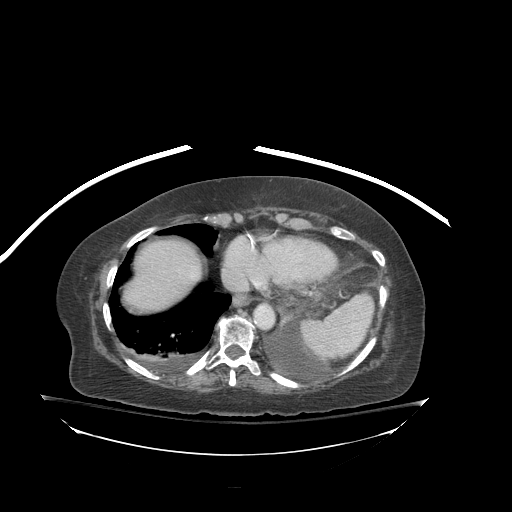
Contrast-enhanced abdominal CT (liver protocol), one axial slice. Position 77 of 81 along the scan axis. Soft-tissue window (W 400 / L 40 HU). 512 × 512 image matrix. From the clinical record (not read from this slice): diagnosis: hepatocellular carcinoma (patient treated with transarterial chemoembolisation; whether this scan precedes or follows treatment is not stated here); TNM stage (as recorded): Stage-I; Child-Pugh class: B.
Annotated regions visible in this slice (semi-automatically segmented with operator editing):
- abdominal aorta: bounding box [x1, y1, x2, y2] px = [255, 304, 273, 326]
- liver parenchyma outside the tumour (the mass and vessels are separate outlines, so this box may not span the whole liver): [124, 240, 202, 312]
- liver vessels: [190, 274, 196, 278]